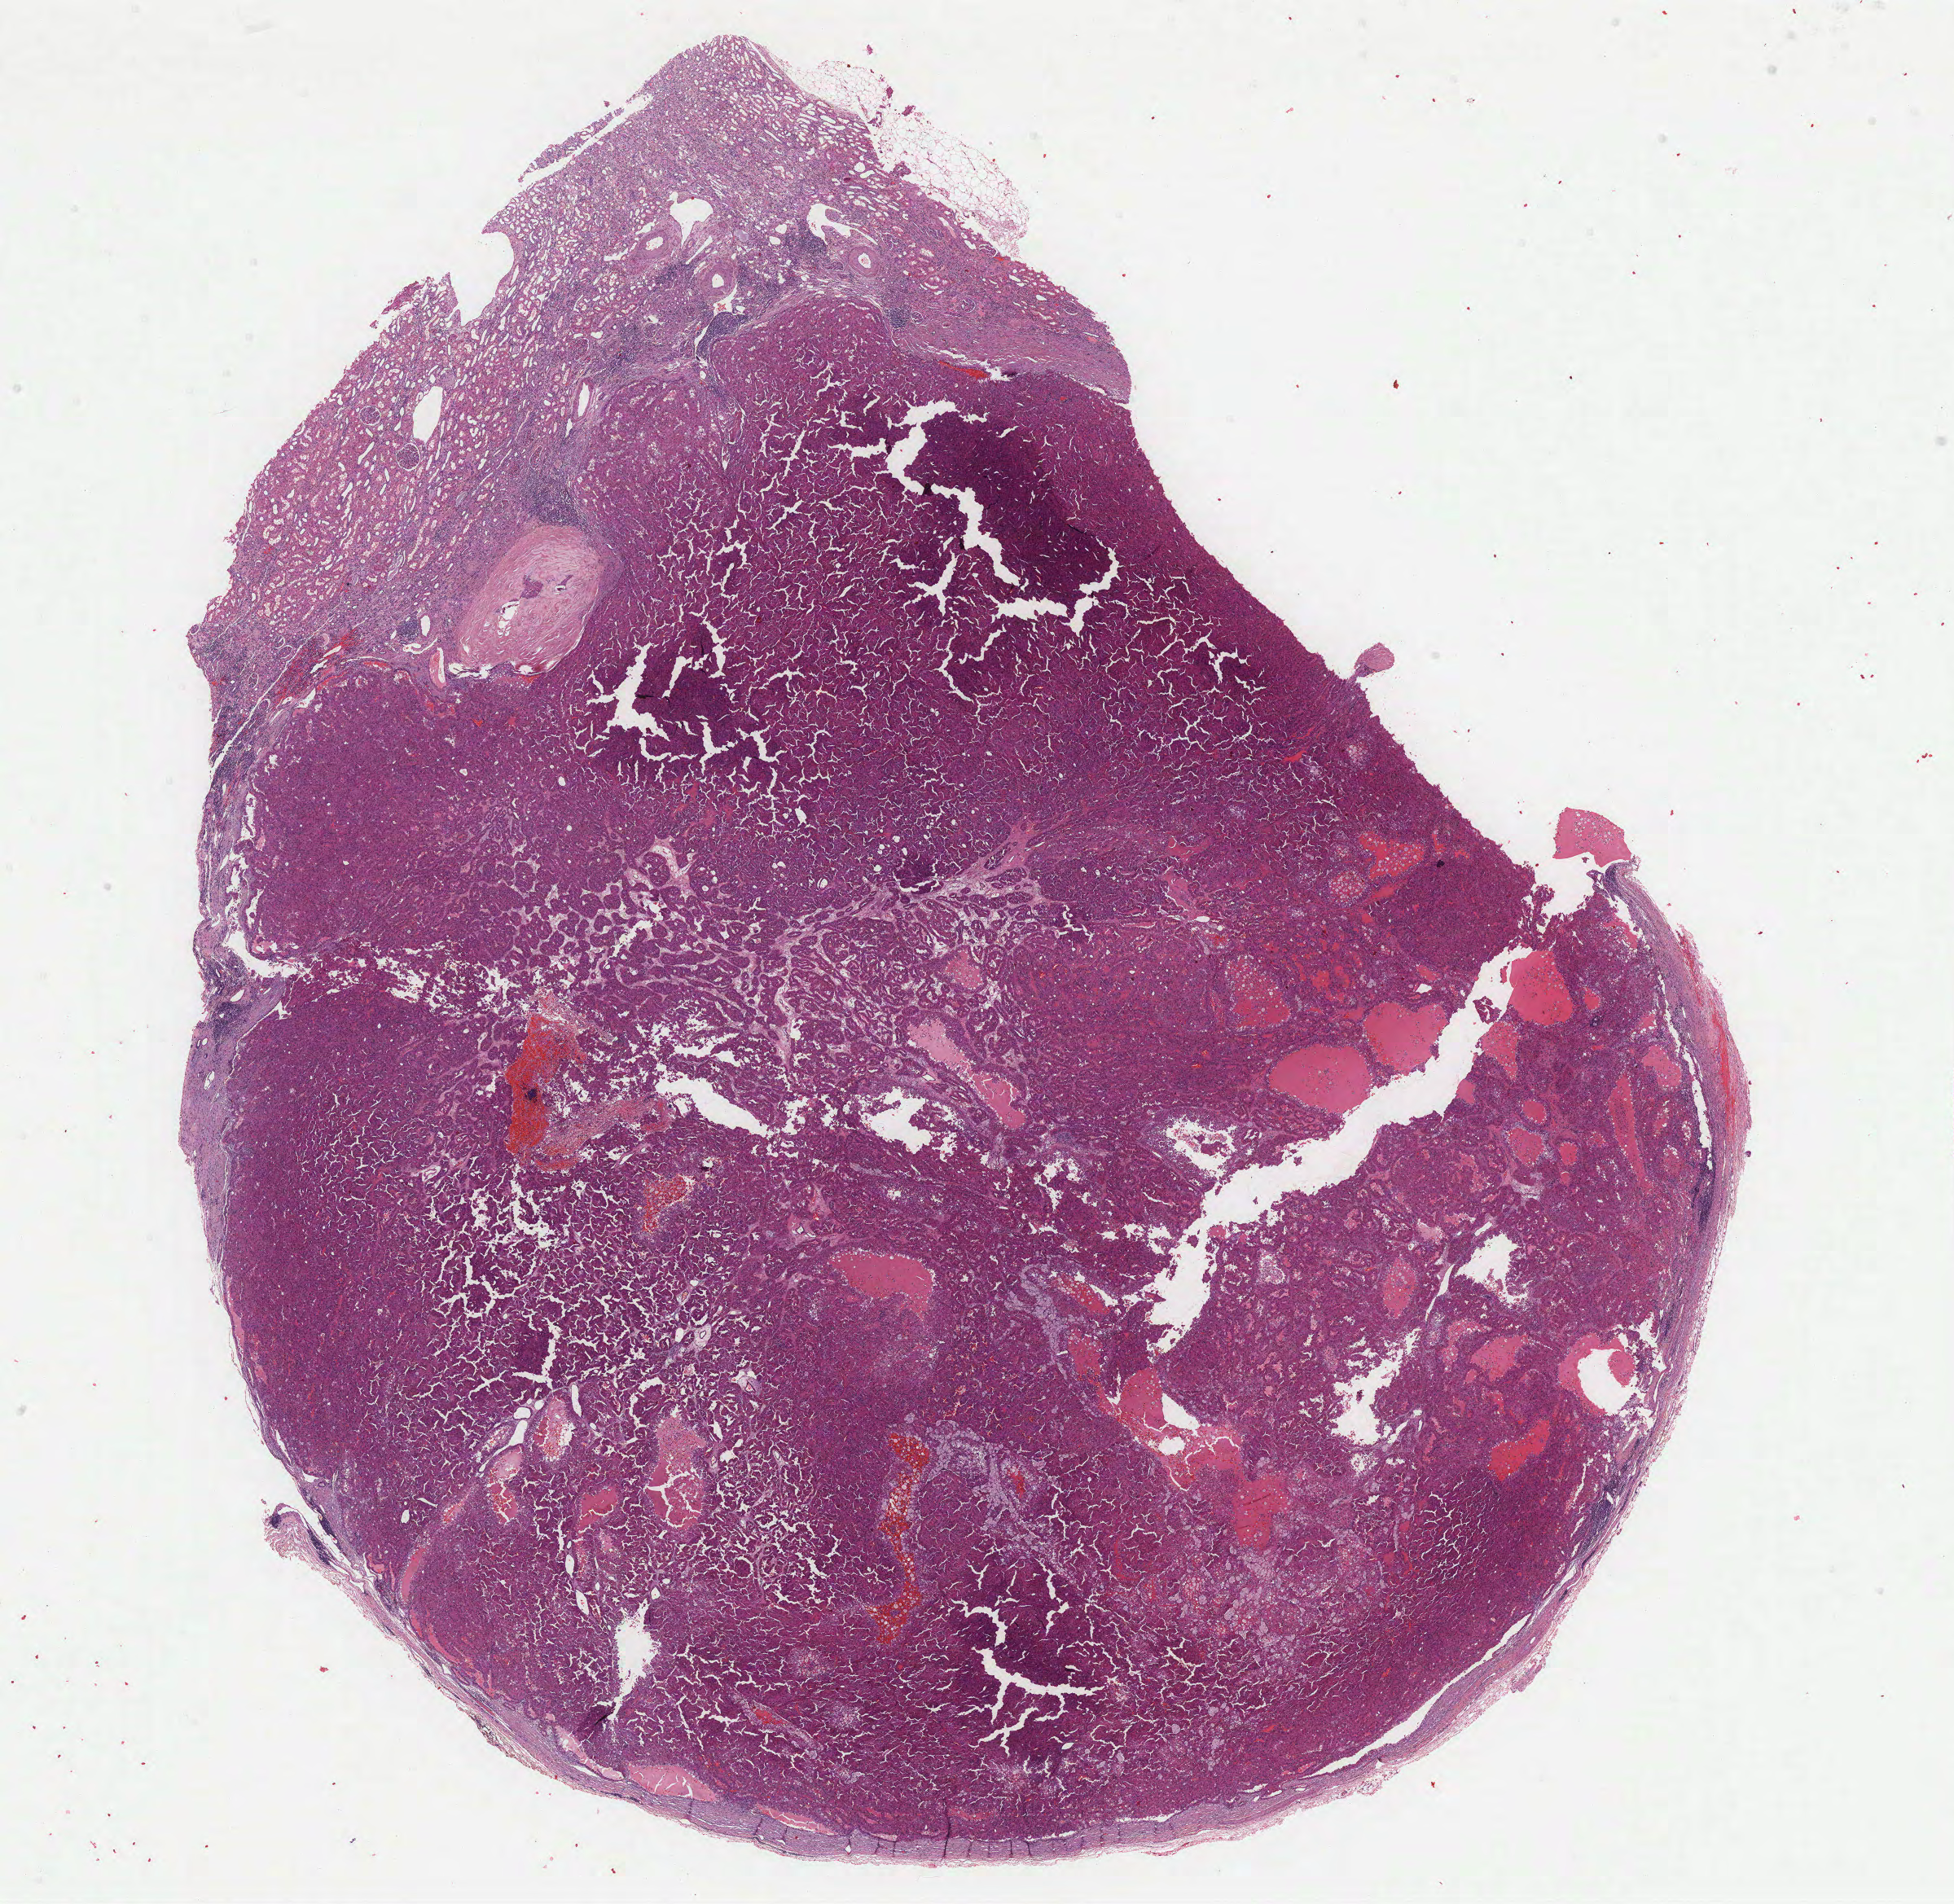
Hematoxylin and eosin (H&E) stained whole-slide image — whole scanned area (about 19.4 x 18.9 mm, slide scanned at 40x) shown as a low-resolution overview; FFPE section; sample: primary tumour, kidney. Female patient; age at initial diagnosis 71 years.
AJCC pathologic stage: I (6th edition). Laterality: left. TNM: T1a NX MX. Diagnosis: Papillary adenocarcinoma, NOS.